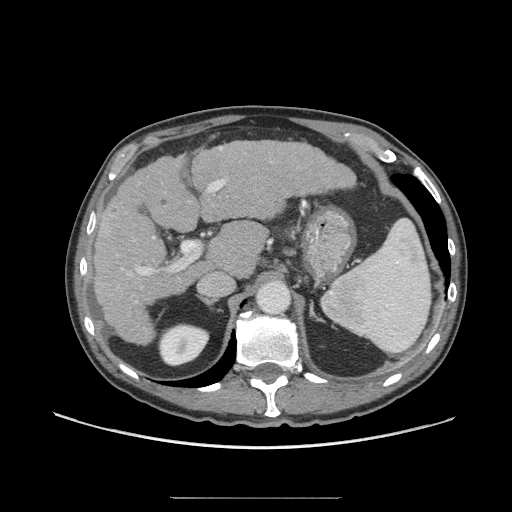
Contrast-enhanced abdominal CT (liver protocol), one axial slice; position 42 of 71 along the scan axis; reconstruction kernel STANDARD; soft-tissue window (W 400 / L 40 HU); 2.5 mm slice thickness; 512 × 512 image matrix, field of view 400 × 400 mm. Case-level facts recorded for this patient, not image findings: diagnosis: hepatocellular carcinoma (patient treated with transarterial chemoembolisation; whether this scan precedes or follows treatment is not stated here); TNM stage (as recorded): Stage-I; Child-Pugh class: A; tumour differentiation: well differentiated; tumour nodularity: uninodular.
Outlined on this slice (semi-automatic segmentation, software-assisted and operator-edited):
- liver parenchyma outside the tumour (the mass and vessels are separate outlines, so this box may not span the whole liver): bounding box <92,140,354,344> (left, top, right, bottom; pixels)
- liver vessels: <111,147,226,302>